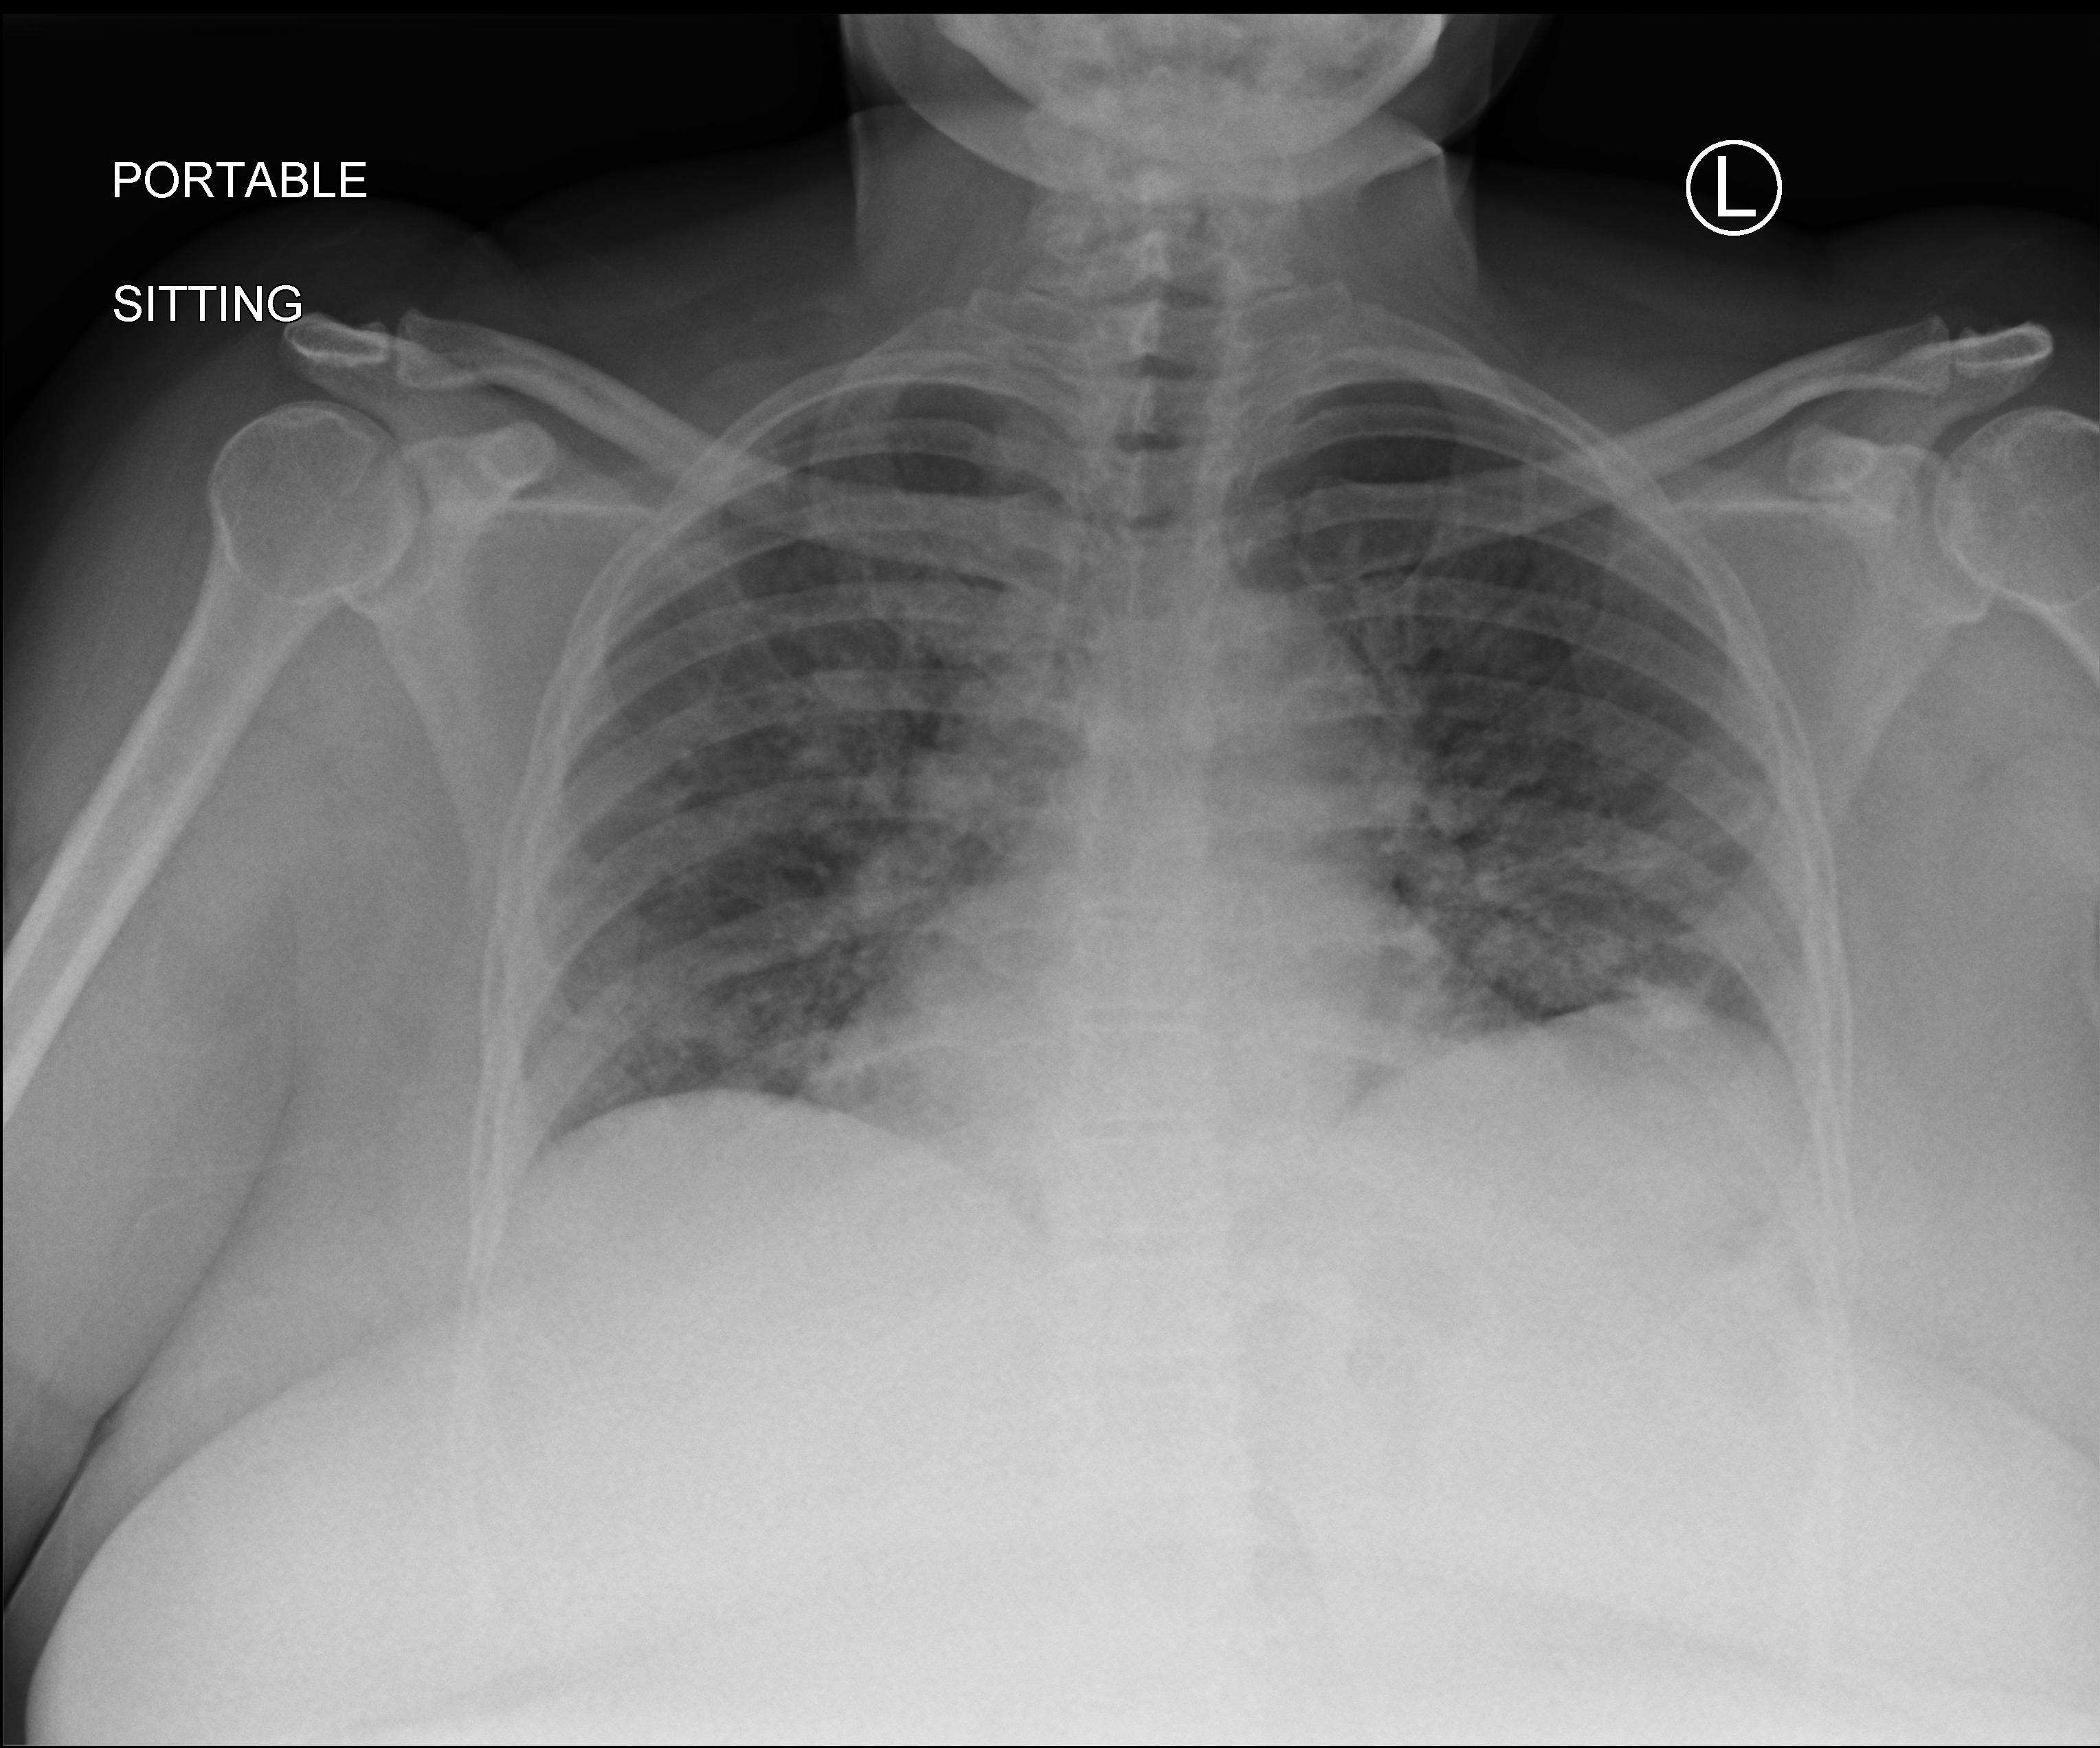
Chest X-ray (portable), anteroposterior (AP) projection. Female patient hospitalised with COVID-19, age 60–74 years.
From the hospital-stay record, not from the radiograph (when in the stay this image was taken is not recorded): length of hospital stay: 5 days.